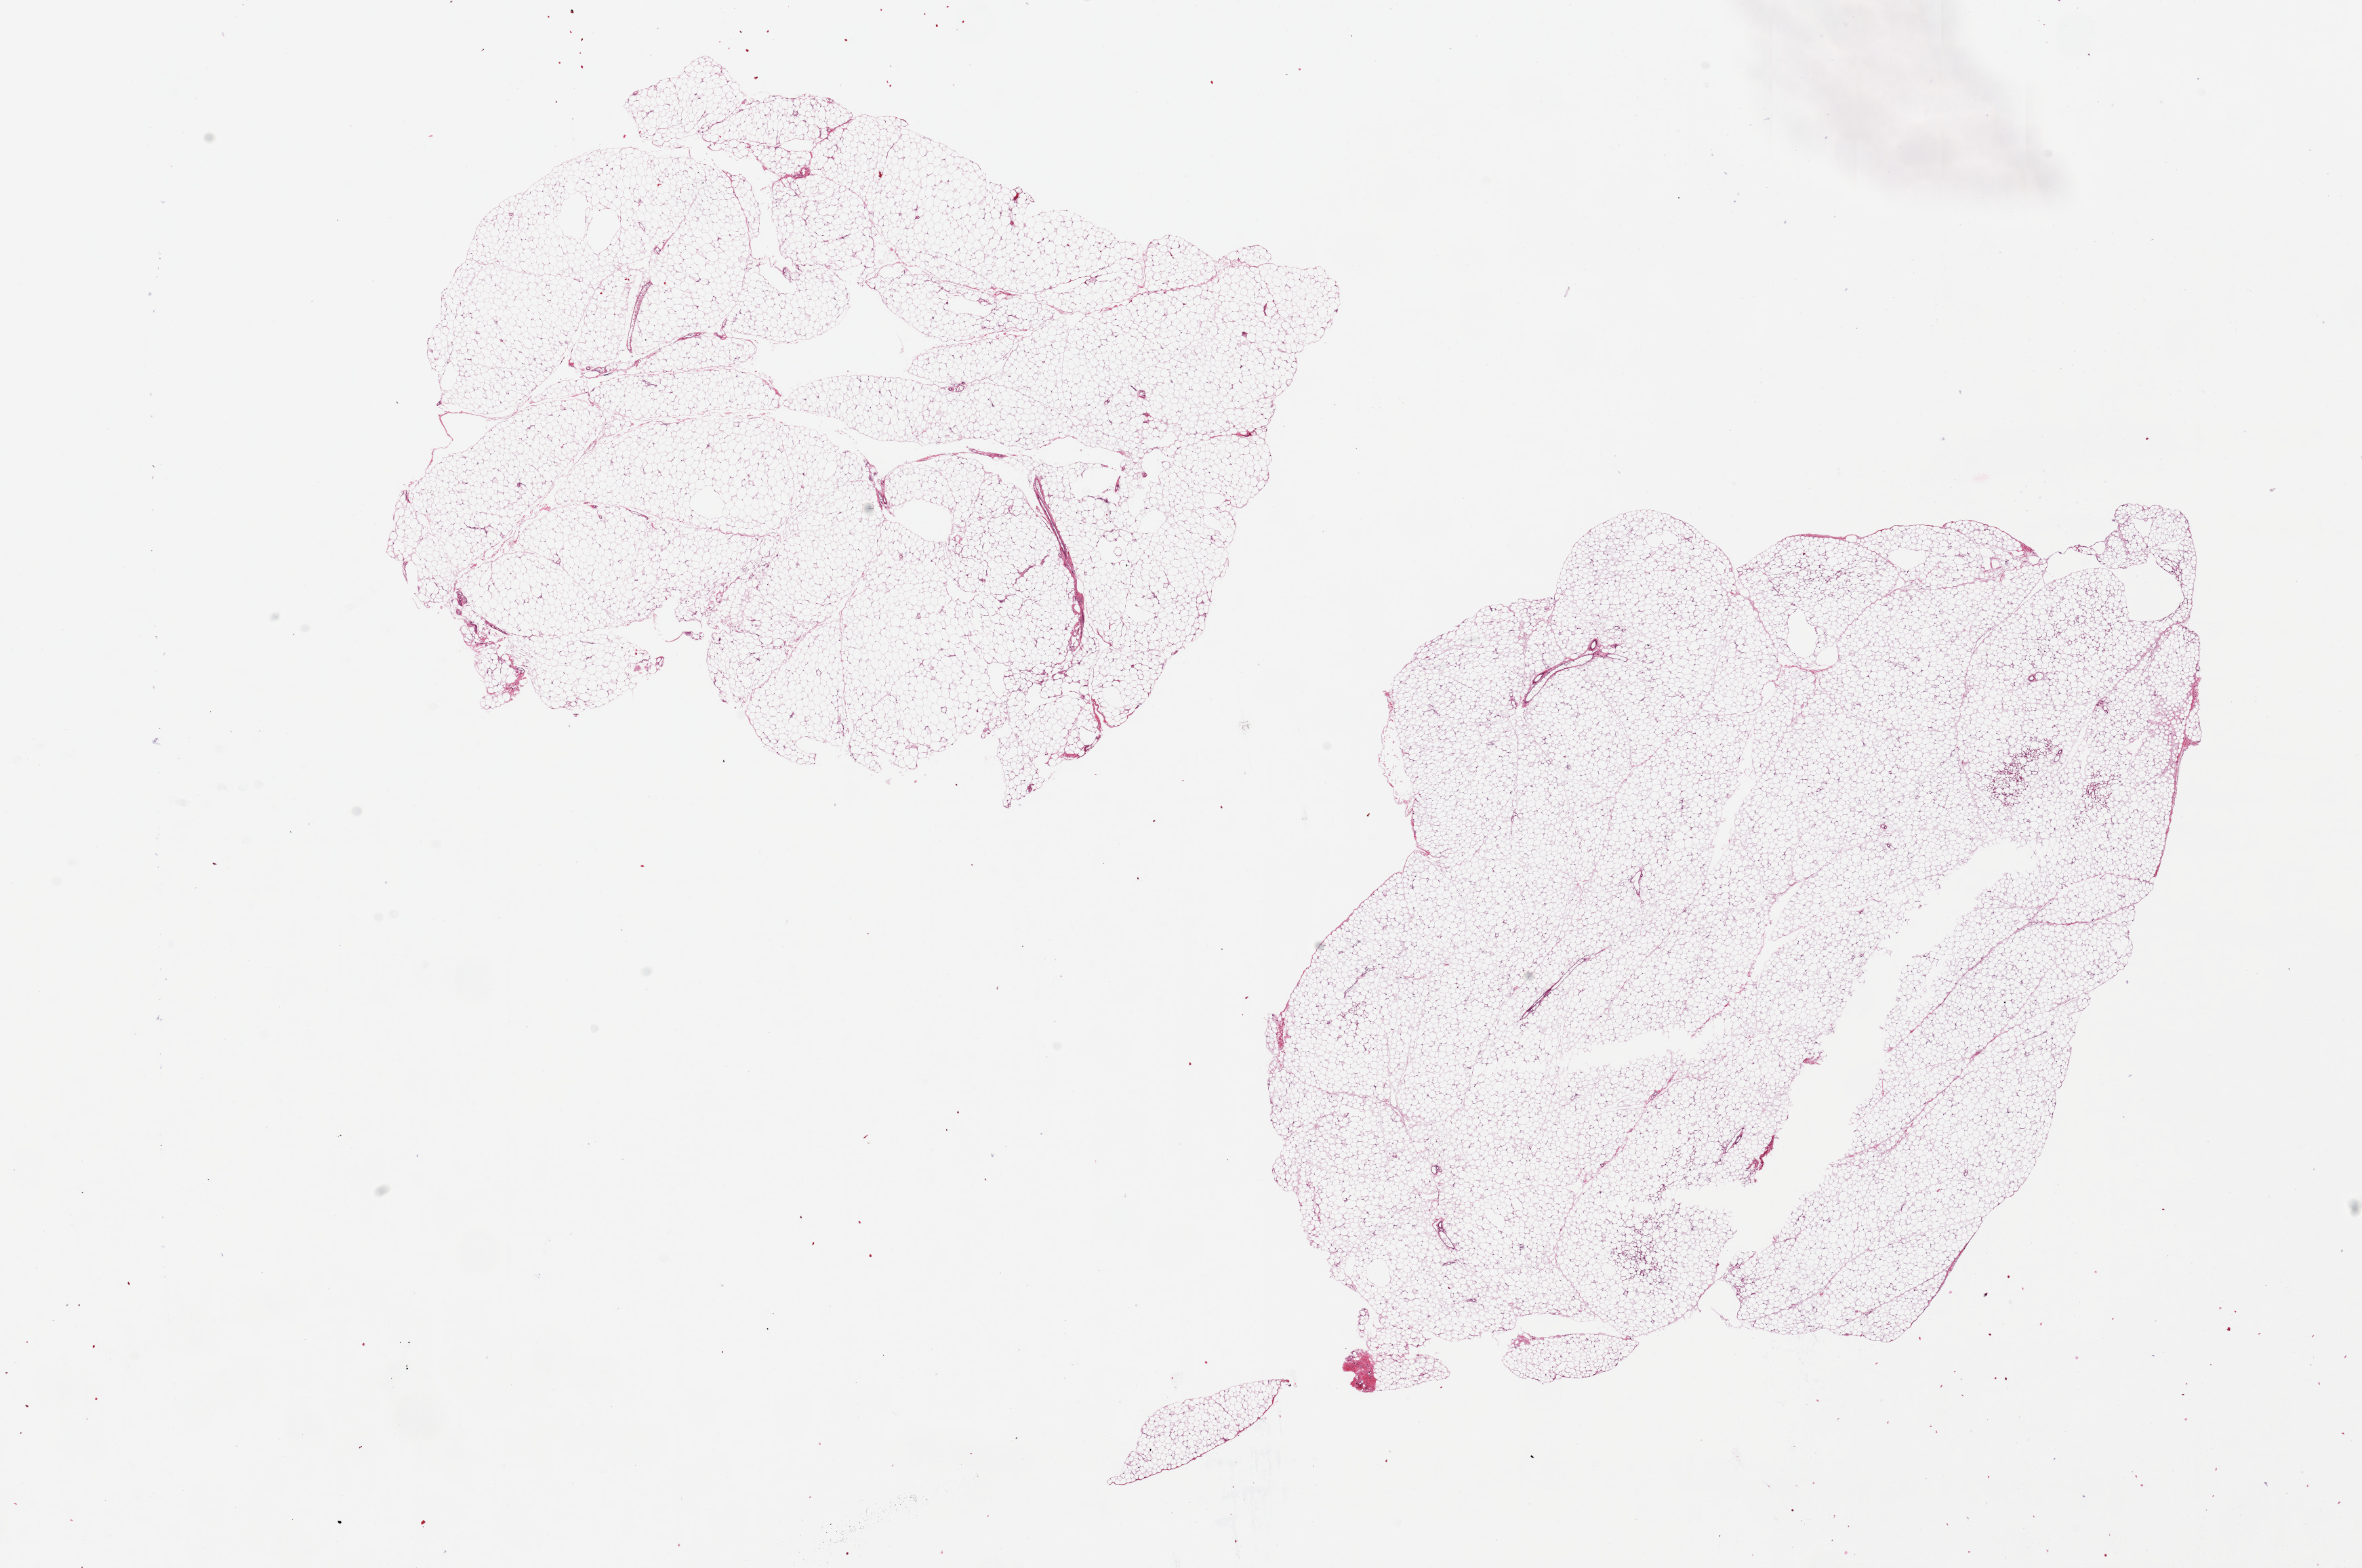
Whole-slide image, H&E stain, brightfield, low-resolution overview of the scanned area, about 27.6 x 18.3 mm (slide scanned at 20x). PAXgene-fixed paraffin-embedded (PFPE) section. Sampled site (target tissue): omentum. Tissue donor sample. Donor sex: male.
• pathologist's review note for this sample: 2 pieces ~9x8mm